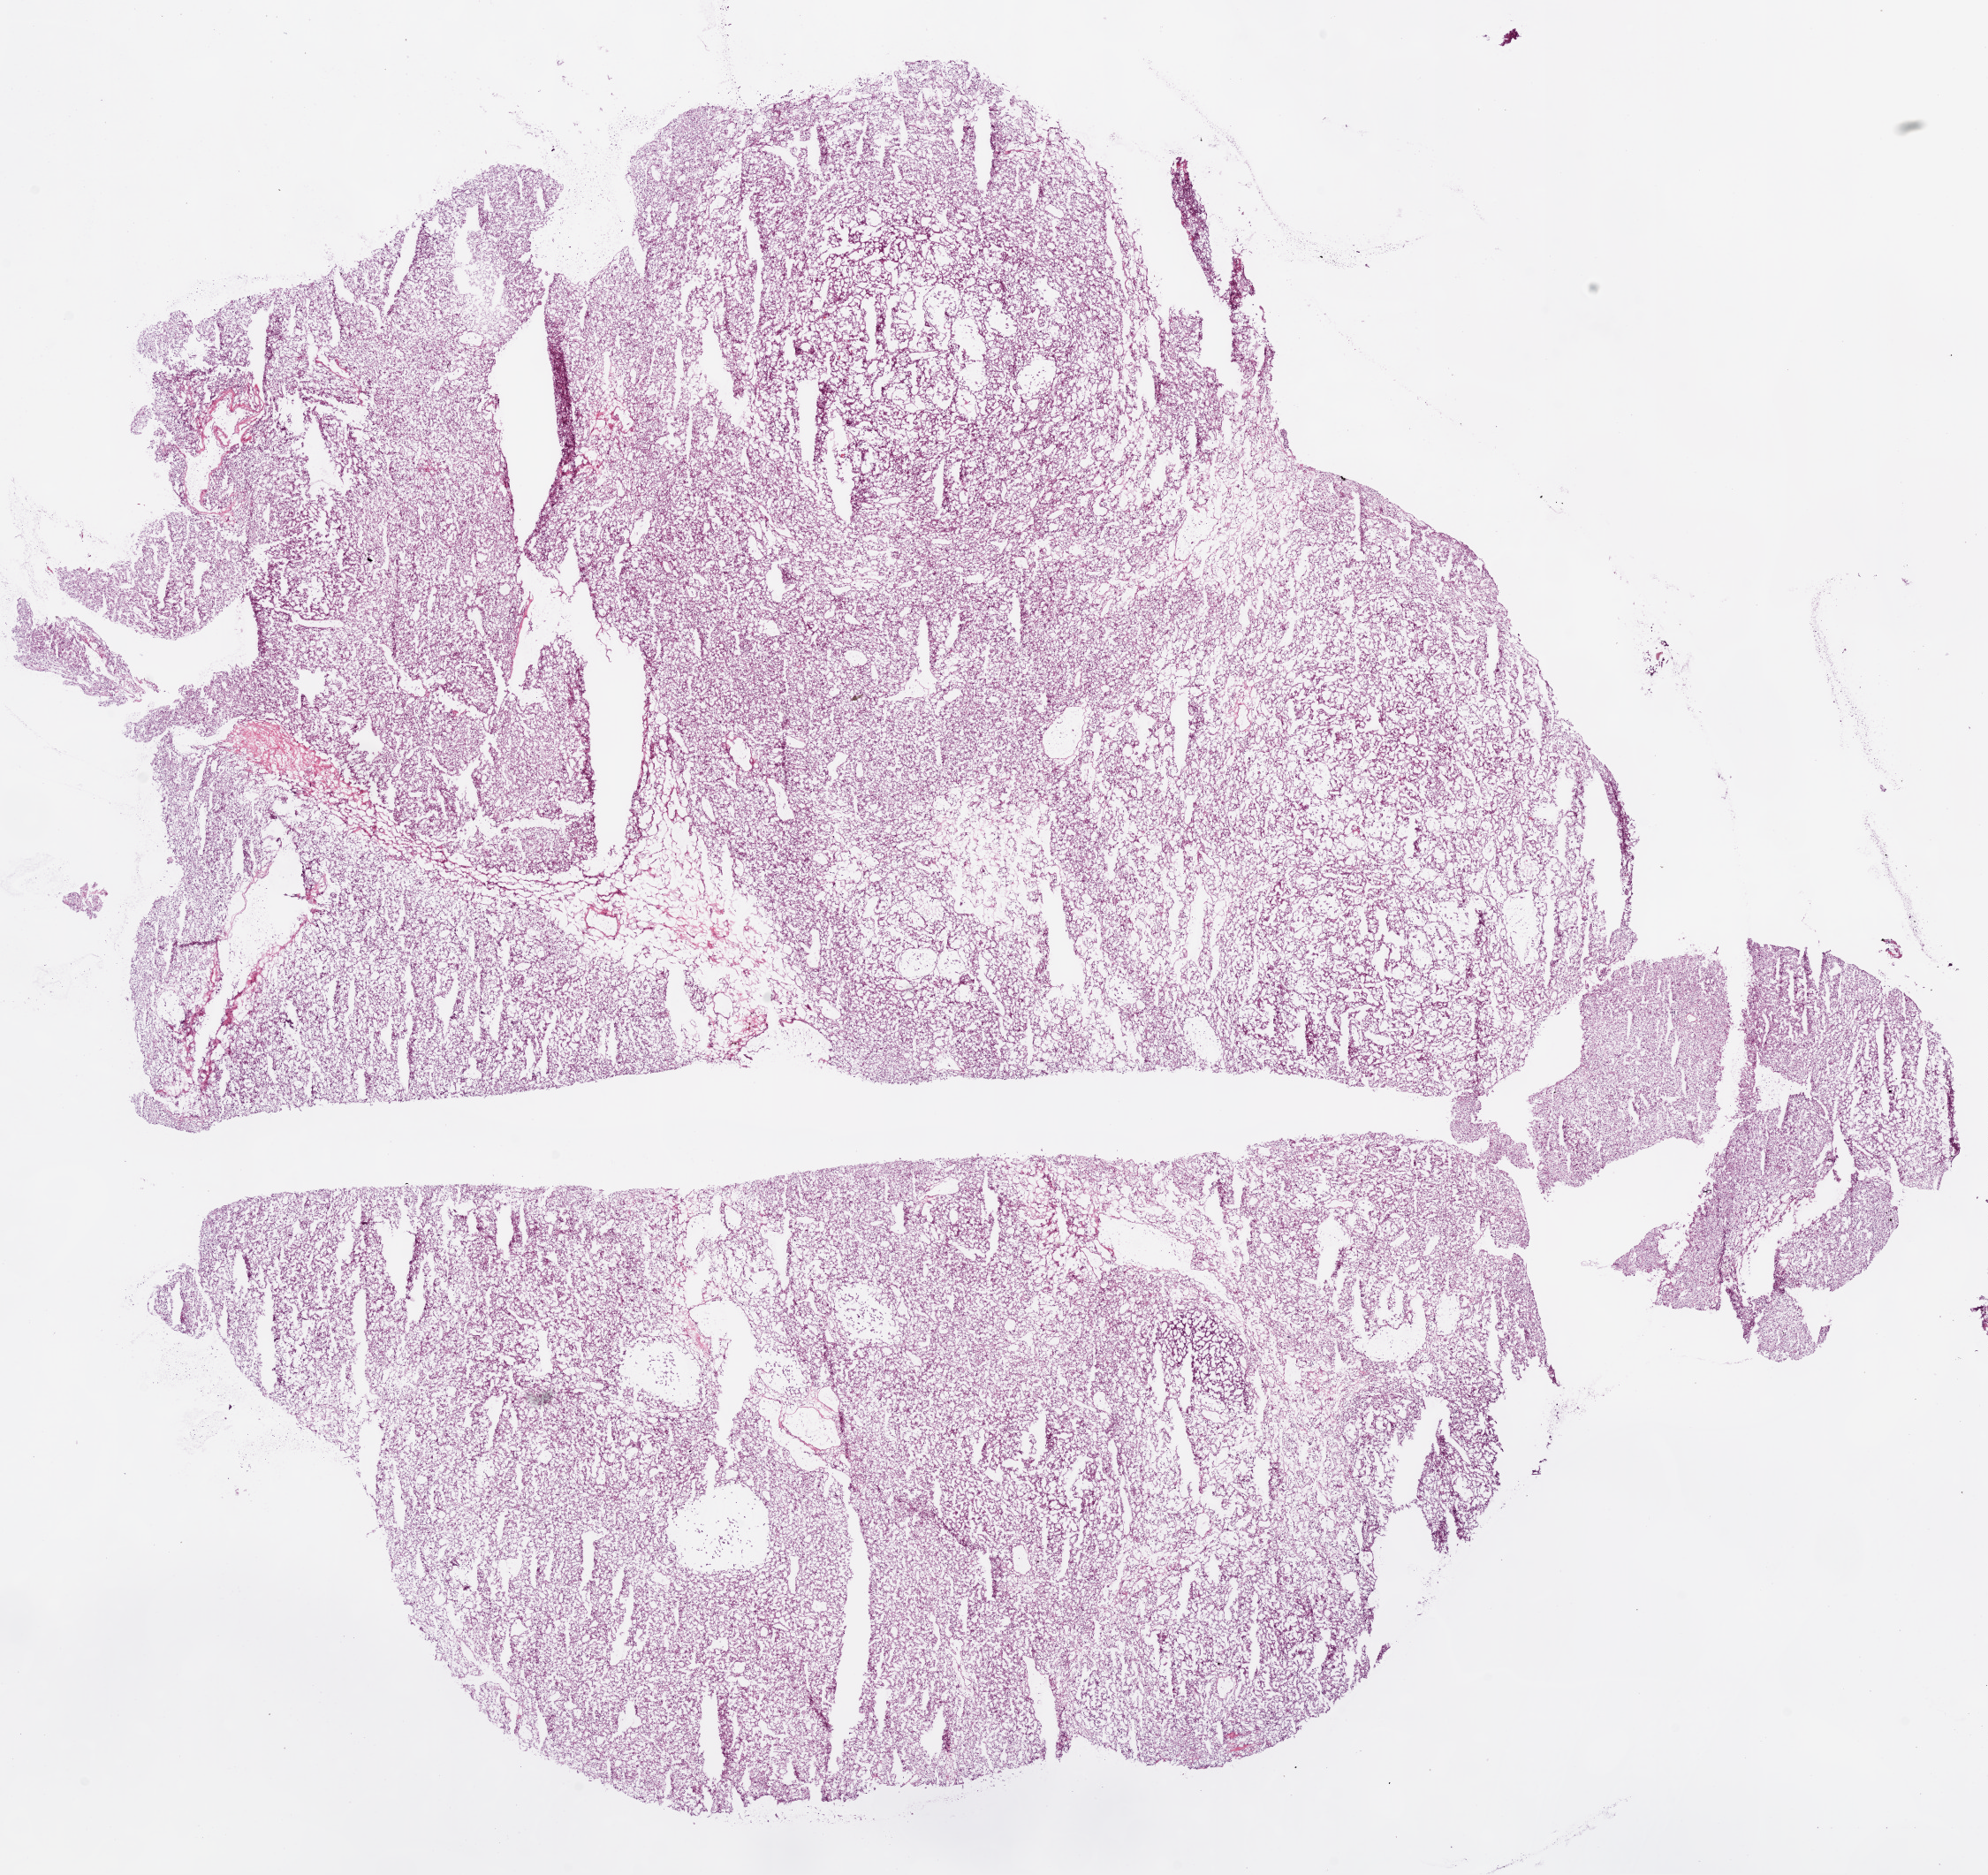
Digitized H&E tissue section (whole slide), a low-resolution overview of the entire scanned area, about 18.1 x 17.0 mm, frozen section from the bottom of the tissue portion, kidney, primary tumour sample. Patient: female, age at initial diagnosis 76 years. Pathologist review of this section (percent, as recorded): tumour cells 90%, tumour nuclei 85%.
Diagnosis: Clear cell adenocarcinoma, NOS.